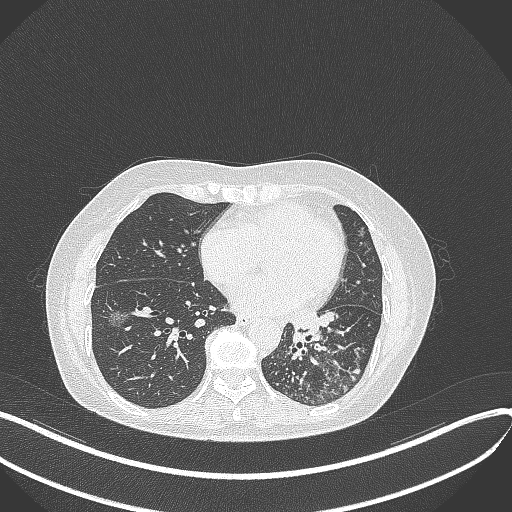
Chest CT, one axial slice; slice 160 of 429 in the series (ordered by position); reconstruction kernel B70f; lung window (W 1500 / L -600 HU); 512 × 512 image matrix, field of view 400 × 400 mm. Patient: female, 63 years. From the clinical record (not read from this slice): clinical TNM (as recorded): T1b N0 M0; histopathological grade: G2-3.
Outlined on this slice (bounding box drawn by a radiologist):
- lung tumour (recorded histology: adenocarcinoma): box from (x=284, y=308) to (x=324, y=344) px